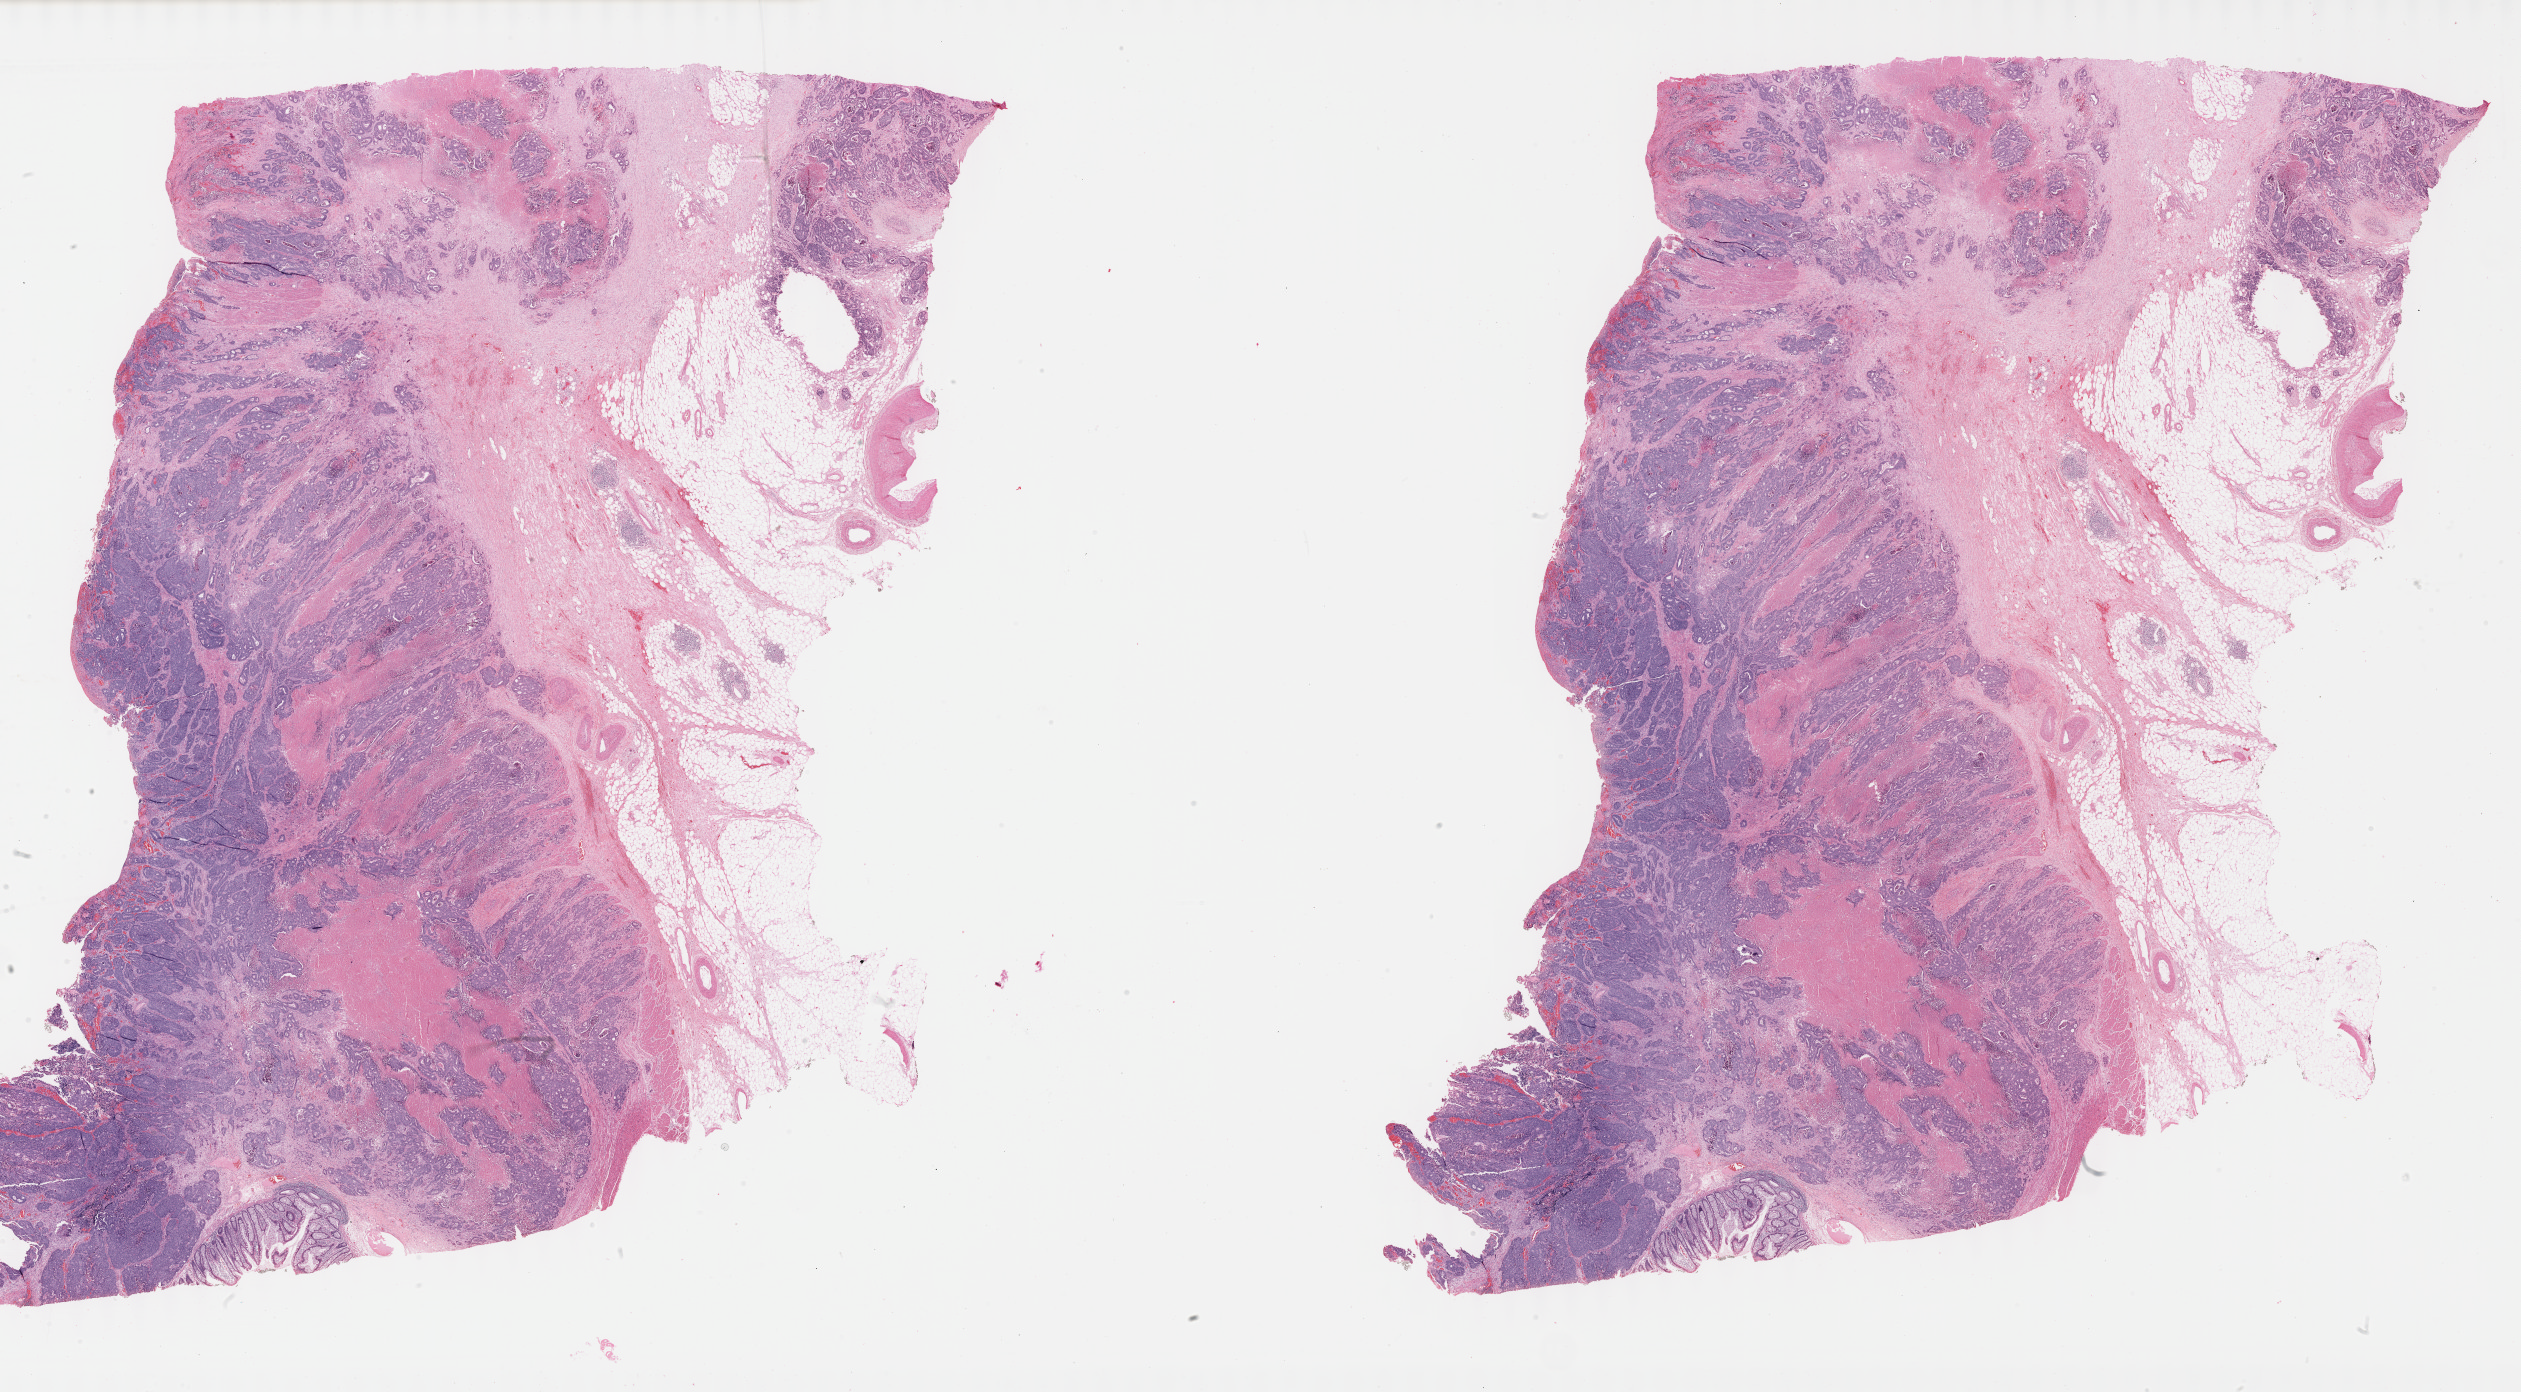
Digitized H&E-stained tissue section (whole slide), whole scanned area (about 40.7 x 22.5 mm) shown as a low-resolution overview.
* specimen: formalin-fixed paraffin-embedded (FFPE) diagnostic section; sample: primary tumour, colon